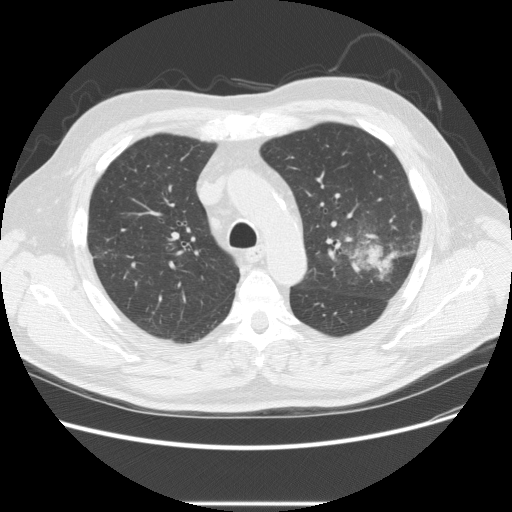
Low-dose screening chest CT, one axial slice; position 164 of 233 along the scan axis; reconstruction kernel STANDARD; 120 kVp; lung window (W 1500 / L -600 HU); 2.5 mm slice thickness; 512 × 512 image matrix, field of view 380 × 380 mm.
Structures marked on this image (expert manual segmentation):
- lesion 1 (tumor, upper lobe of left lung): bounding box [x1, y1, x2, y2] px = [358, 244, 390, 277]